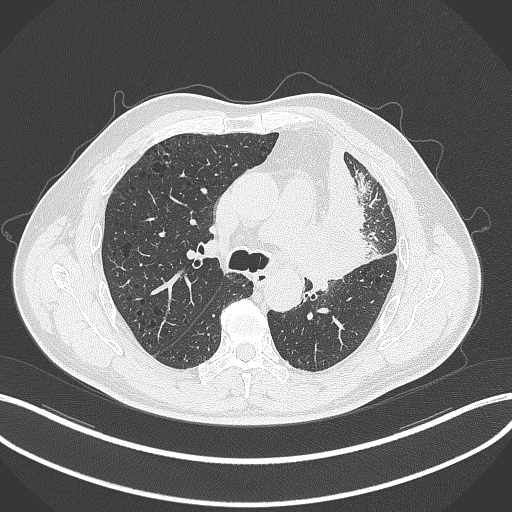
Chest CT, one axial slice. Position 194 of 297 along the scan axis. Lung window (W 1500 / L -600 HU). 1 mm slice thickness. 512 × 512 image matrix. Patient: male, 68 years. Case-level facts recorded for this patient, not image findings: clinical TNM (as recorded): T3 N3 M1.
Structures marked on this image (bounding box drawn by a radiologist):
- lung tumour (recorded histology: adenocarcinoma): bounding box (x1, y1, x2, y2) in pixels: (314, 160, 383, 287)